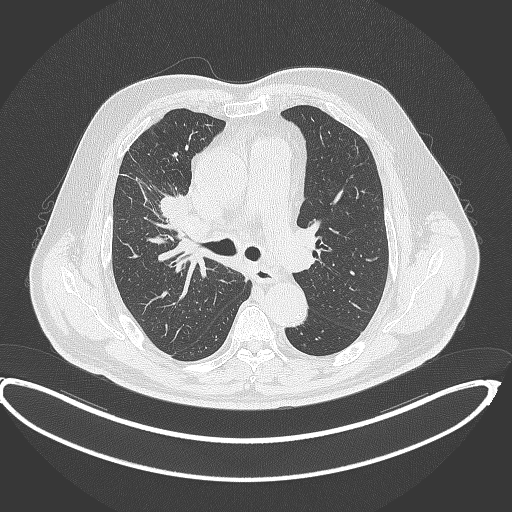
Chest CT, one axial slice. Position 260 of 390 along the scan axis. Lung window (W 1500 / L -600 HU). 1 mm slice thickness. 512 × 512 image matrix, field of view 448 × 448 mm. Male patient, age 62 years. From the clinical record (not read from this slice): clinical TNM (as recorded): T1c N3 M1c.
Outlined on this slice (bounding box drawn by a radiologist):
- lung tumour (recorded histology: adenocarcinoma): bounding box (x1, y1, x2, y2) in pixels: (157, 194, 192, 229)